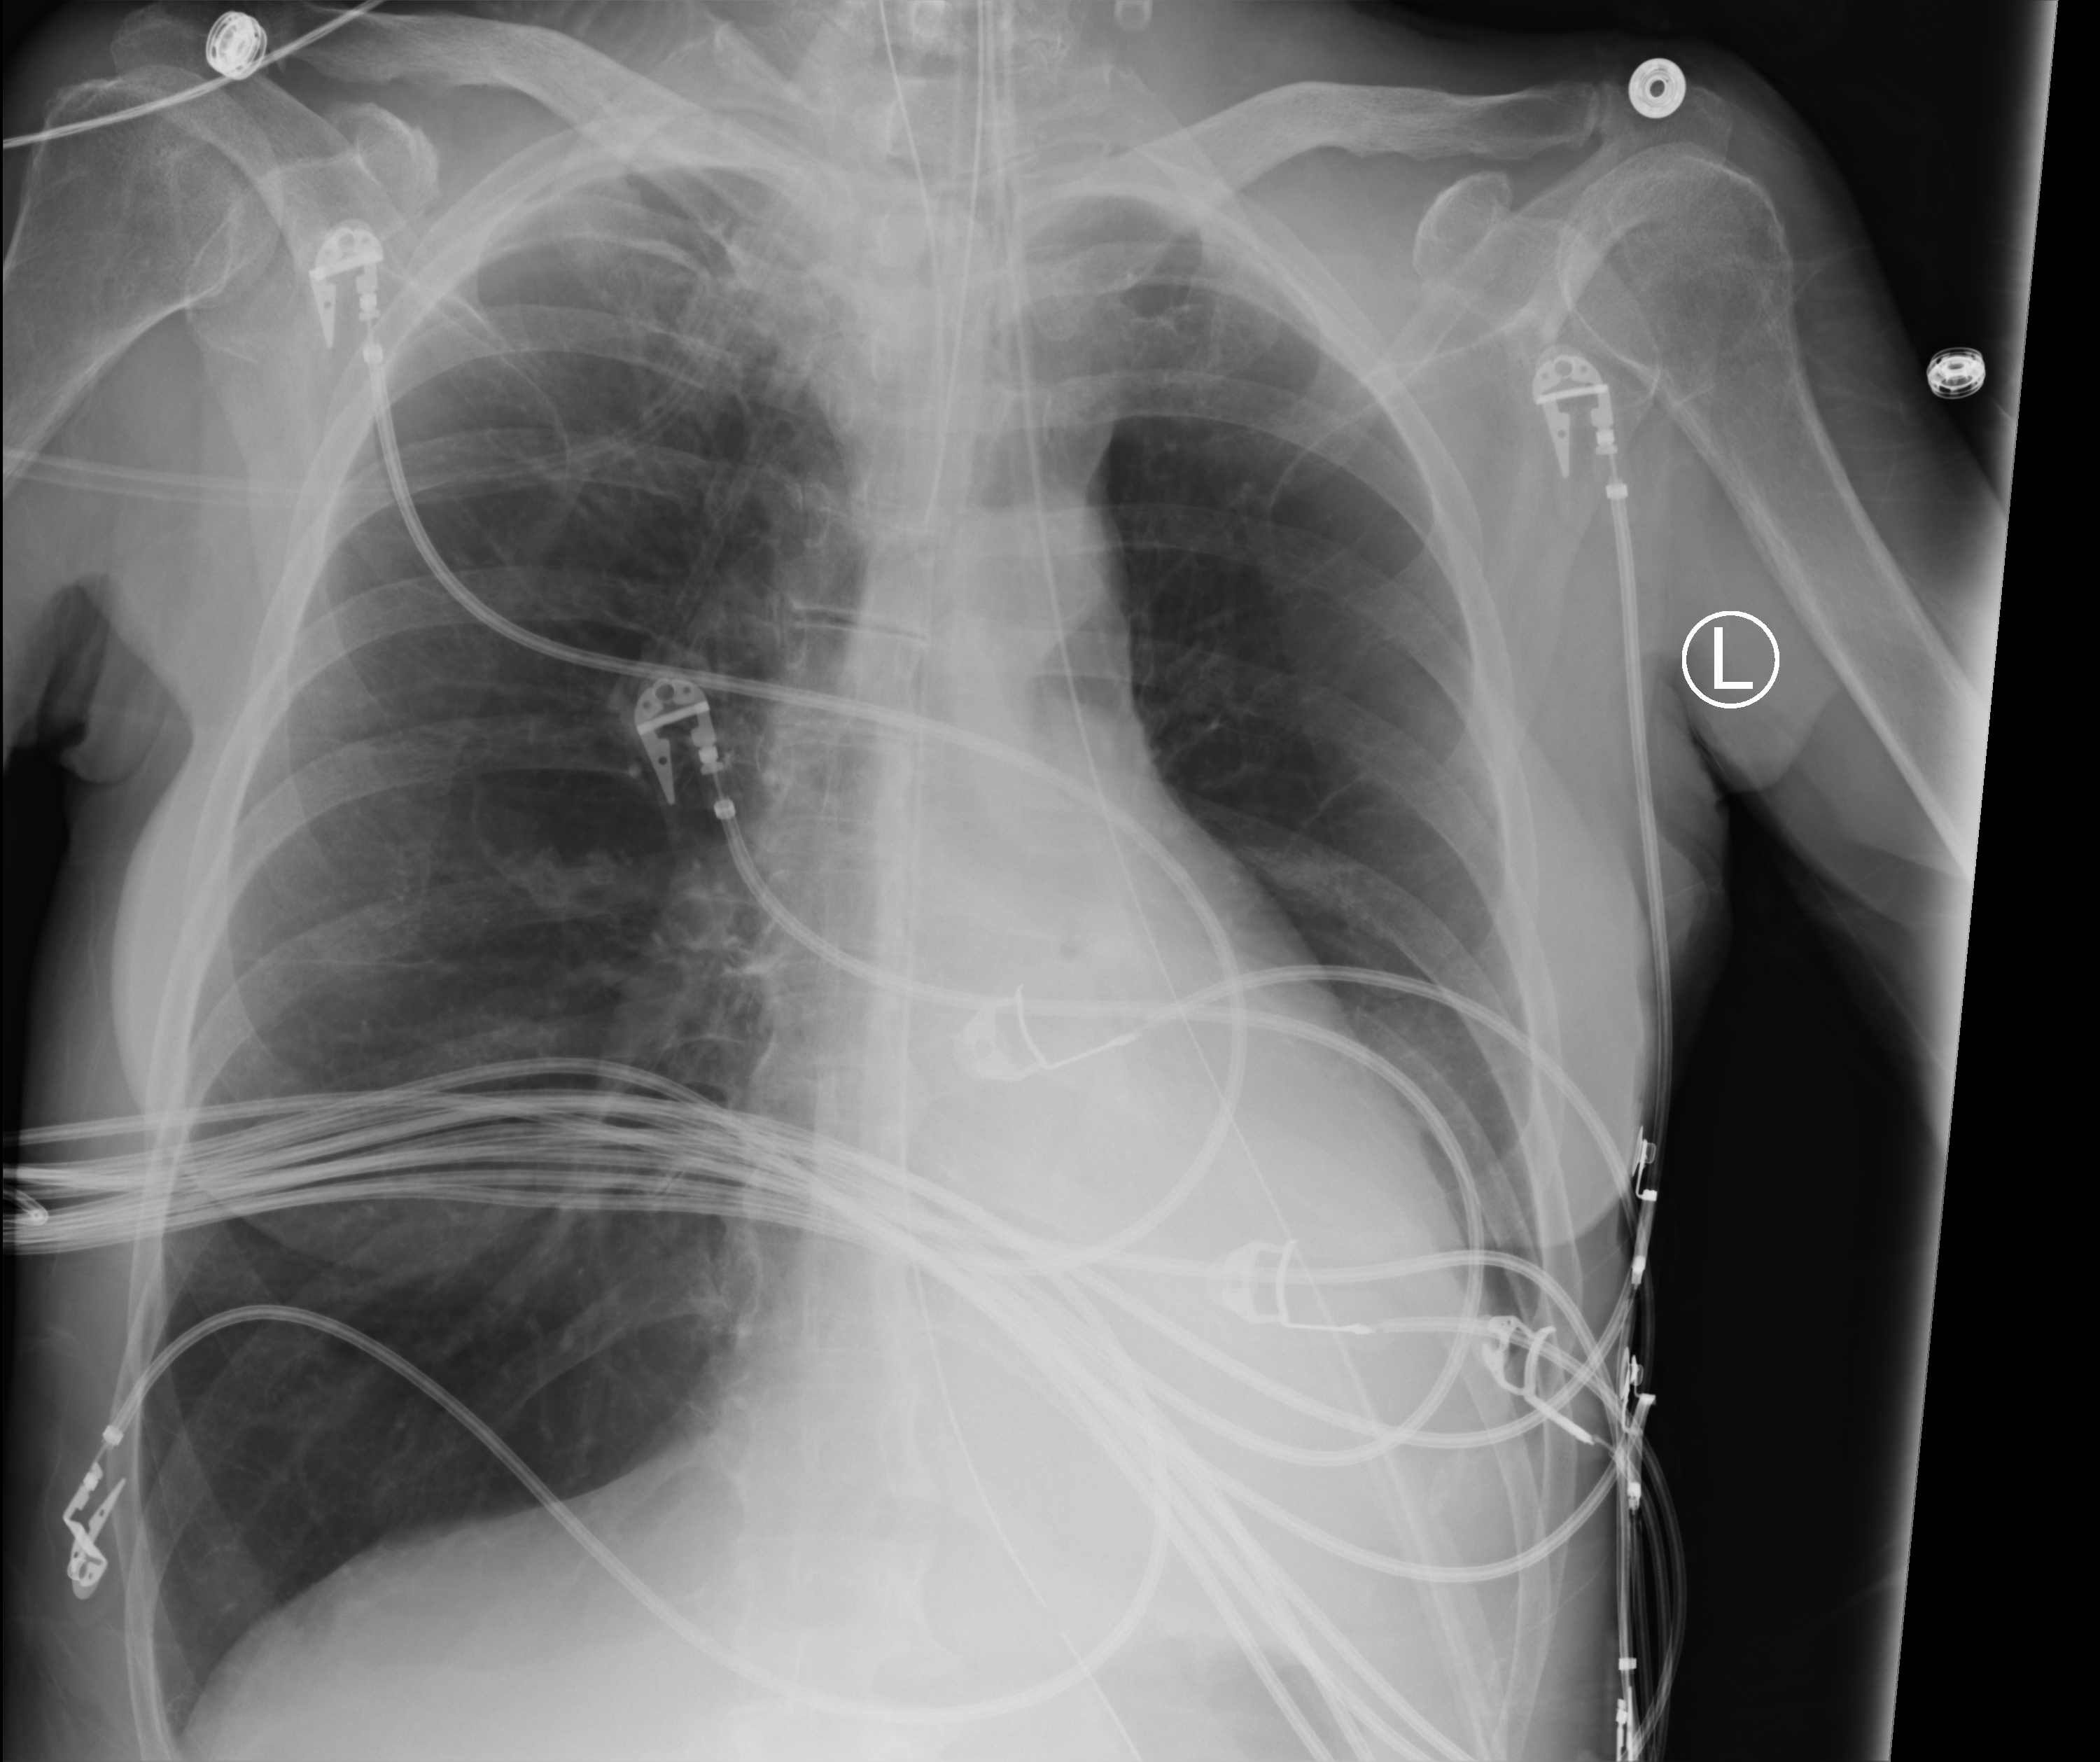
Bedside chest radiograph (computed radiography), anteroposterior (AP) projection. Female patient hospitalised with COVID-19, age 60–74 years.
Hospital-stay facts (about this admission, not read from this image; timing relative to this image not recorded):
- length of hospital stay: 38 days